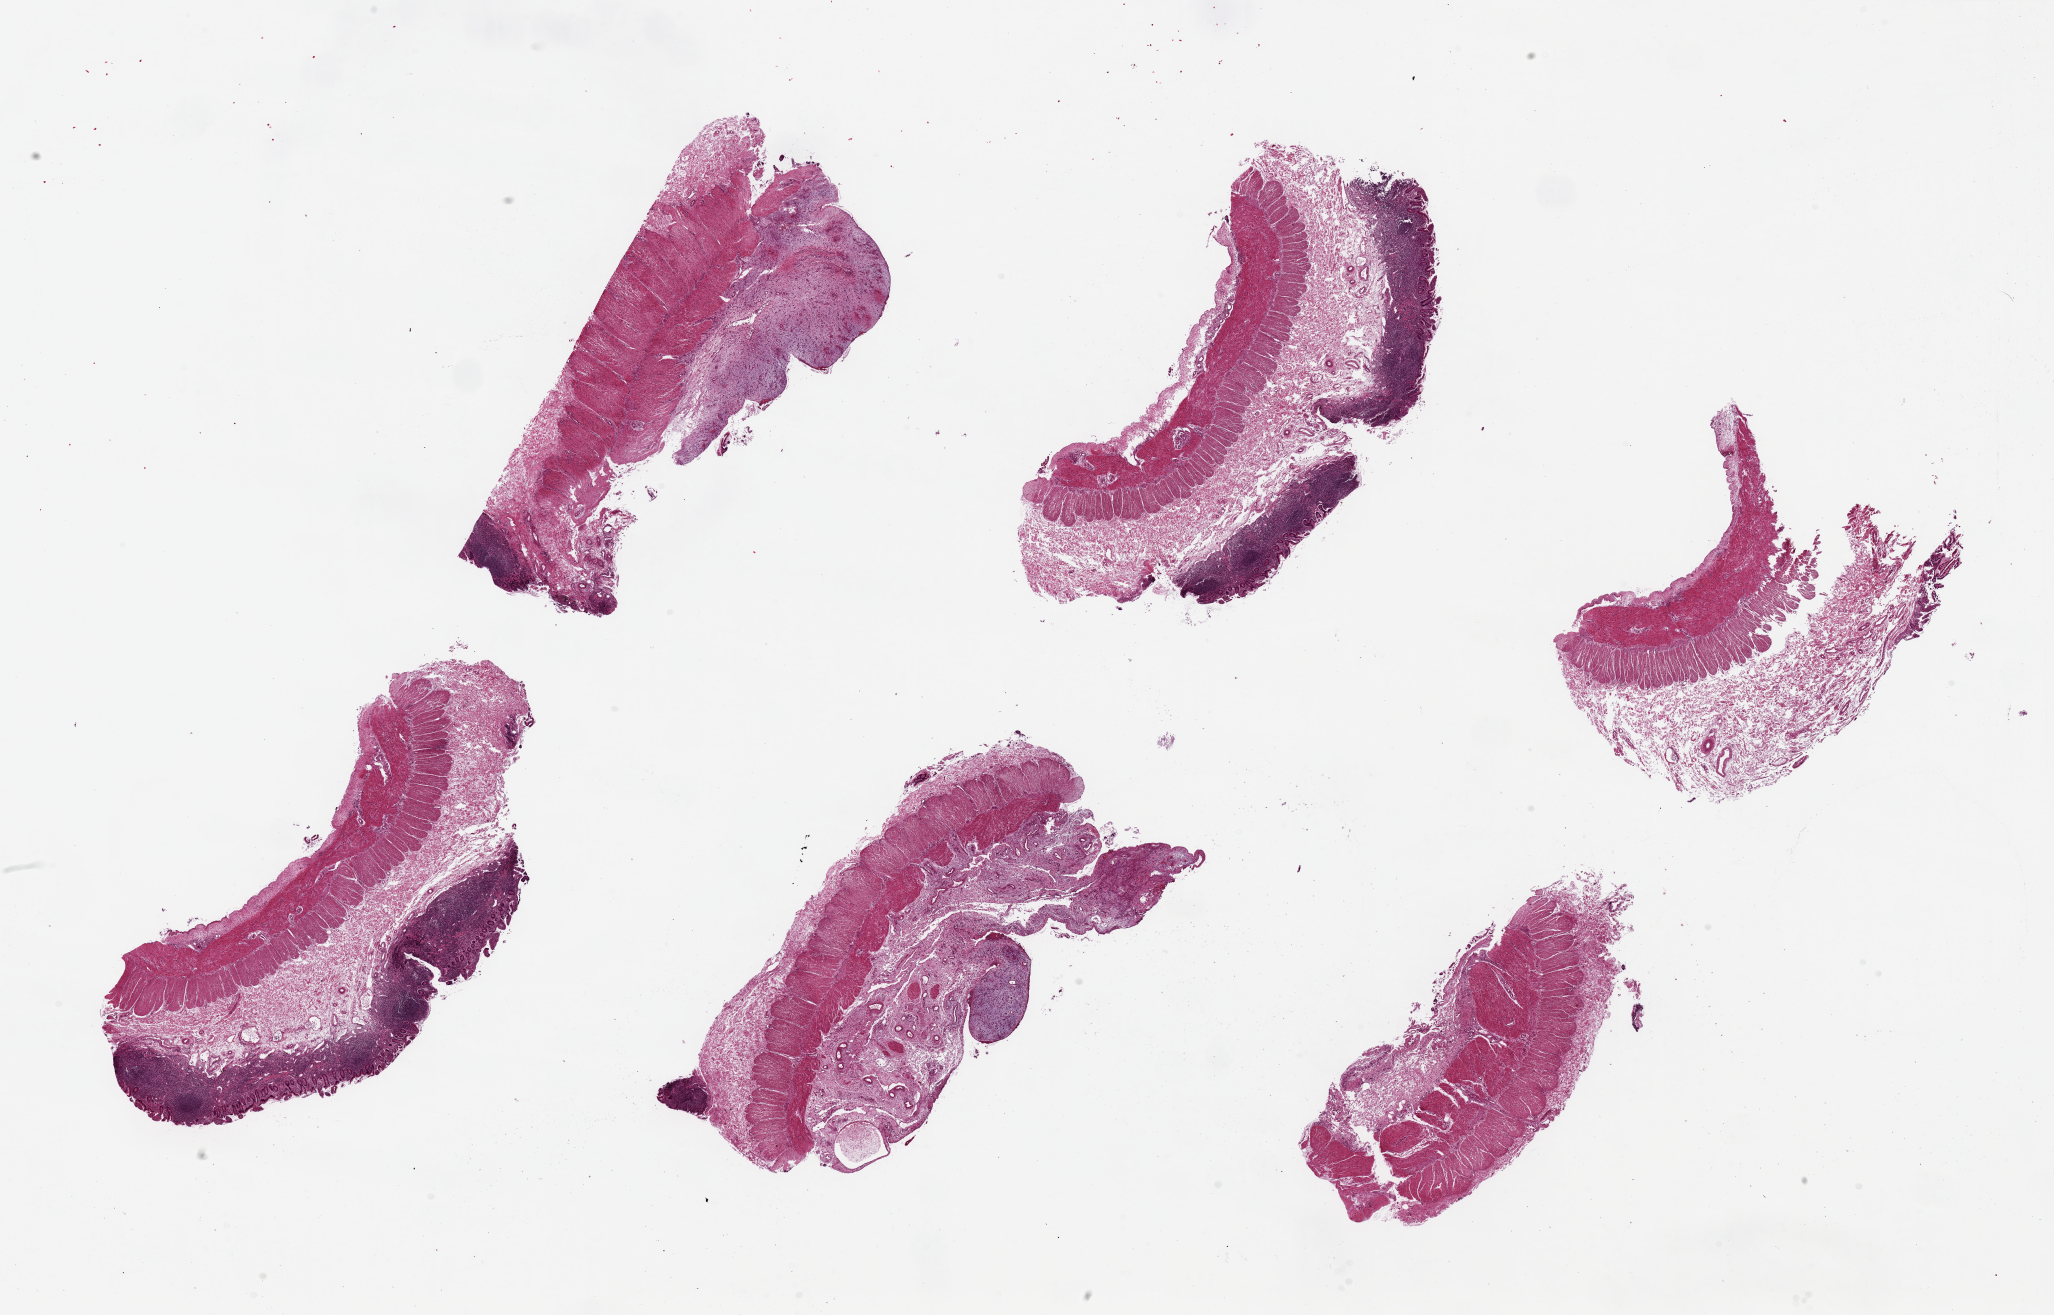
Digitized H&E-stained section — low-resolution overview of the scanned area, about 32.5 x 20.8 mm (slide scanned at 20x). PAXgene-fixed, paraffin-embedded tissue. Sampled site (target tissue): ileum. Tissue donor sample. Donor: male.
Reviewer comment on this tissue sample: 4 pieces ~10% total lymphoid elements.